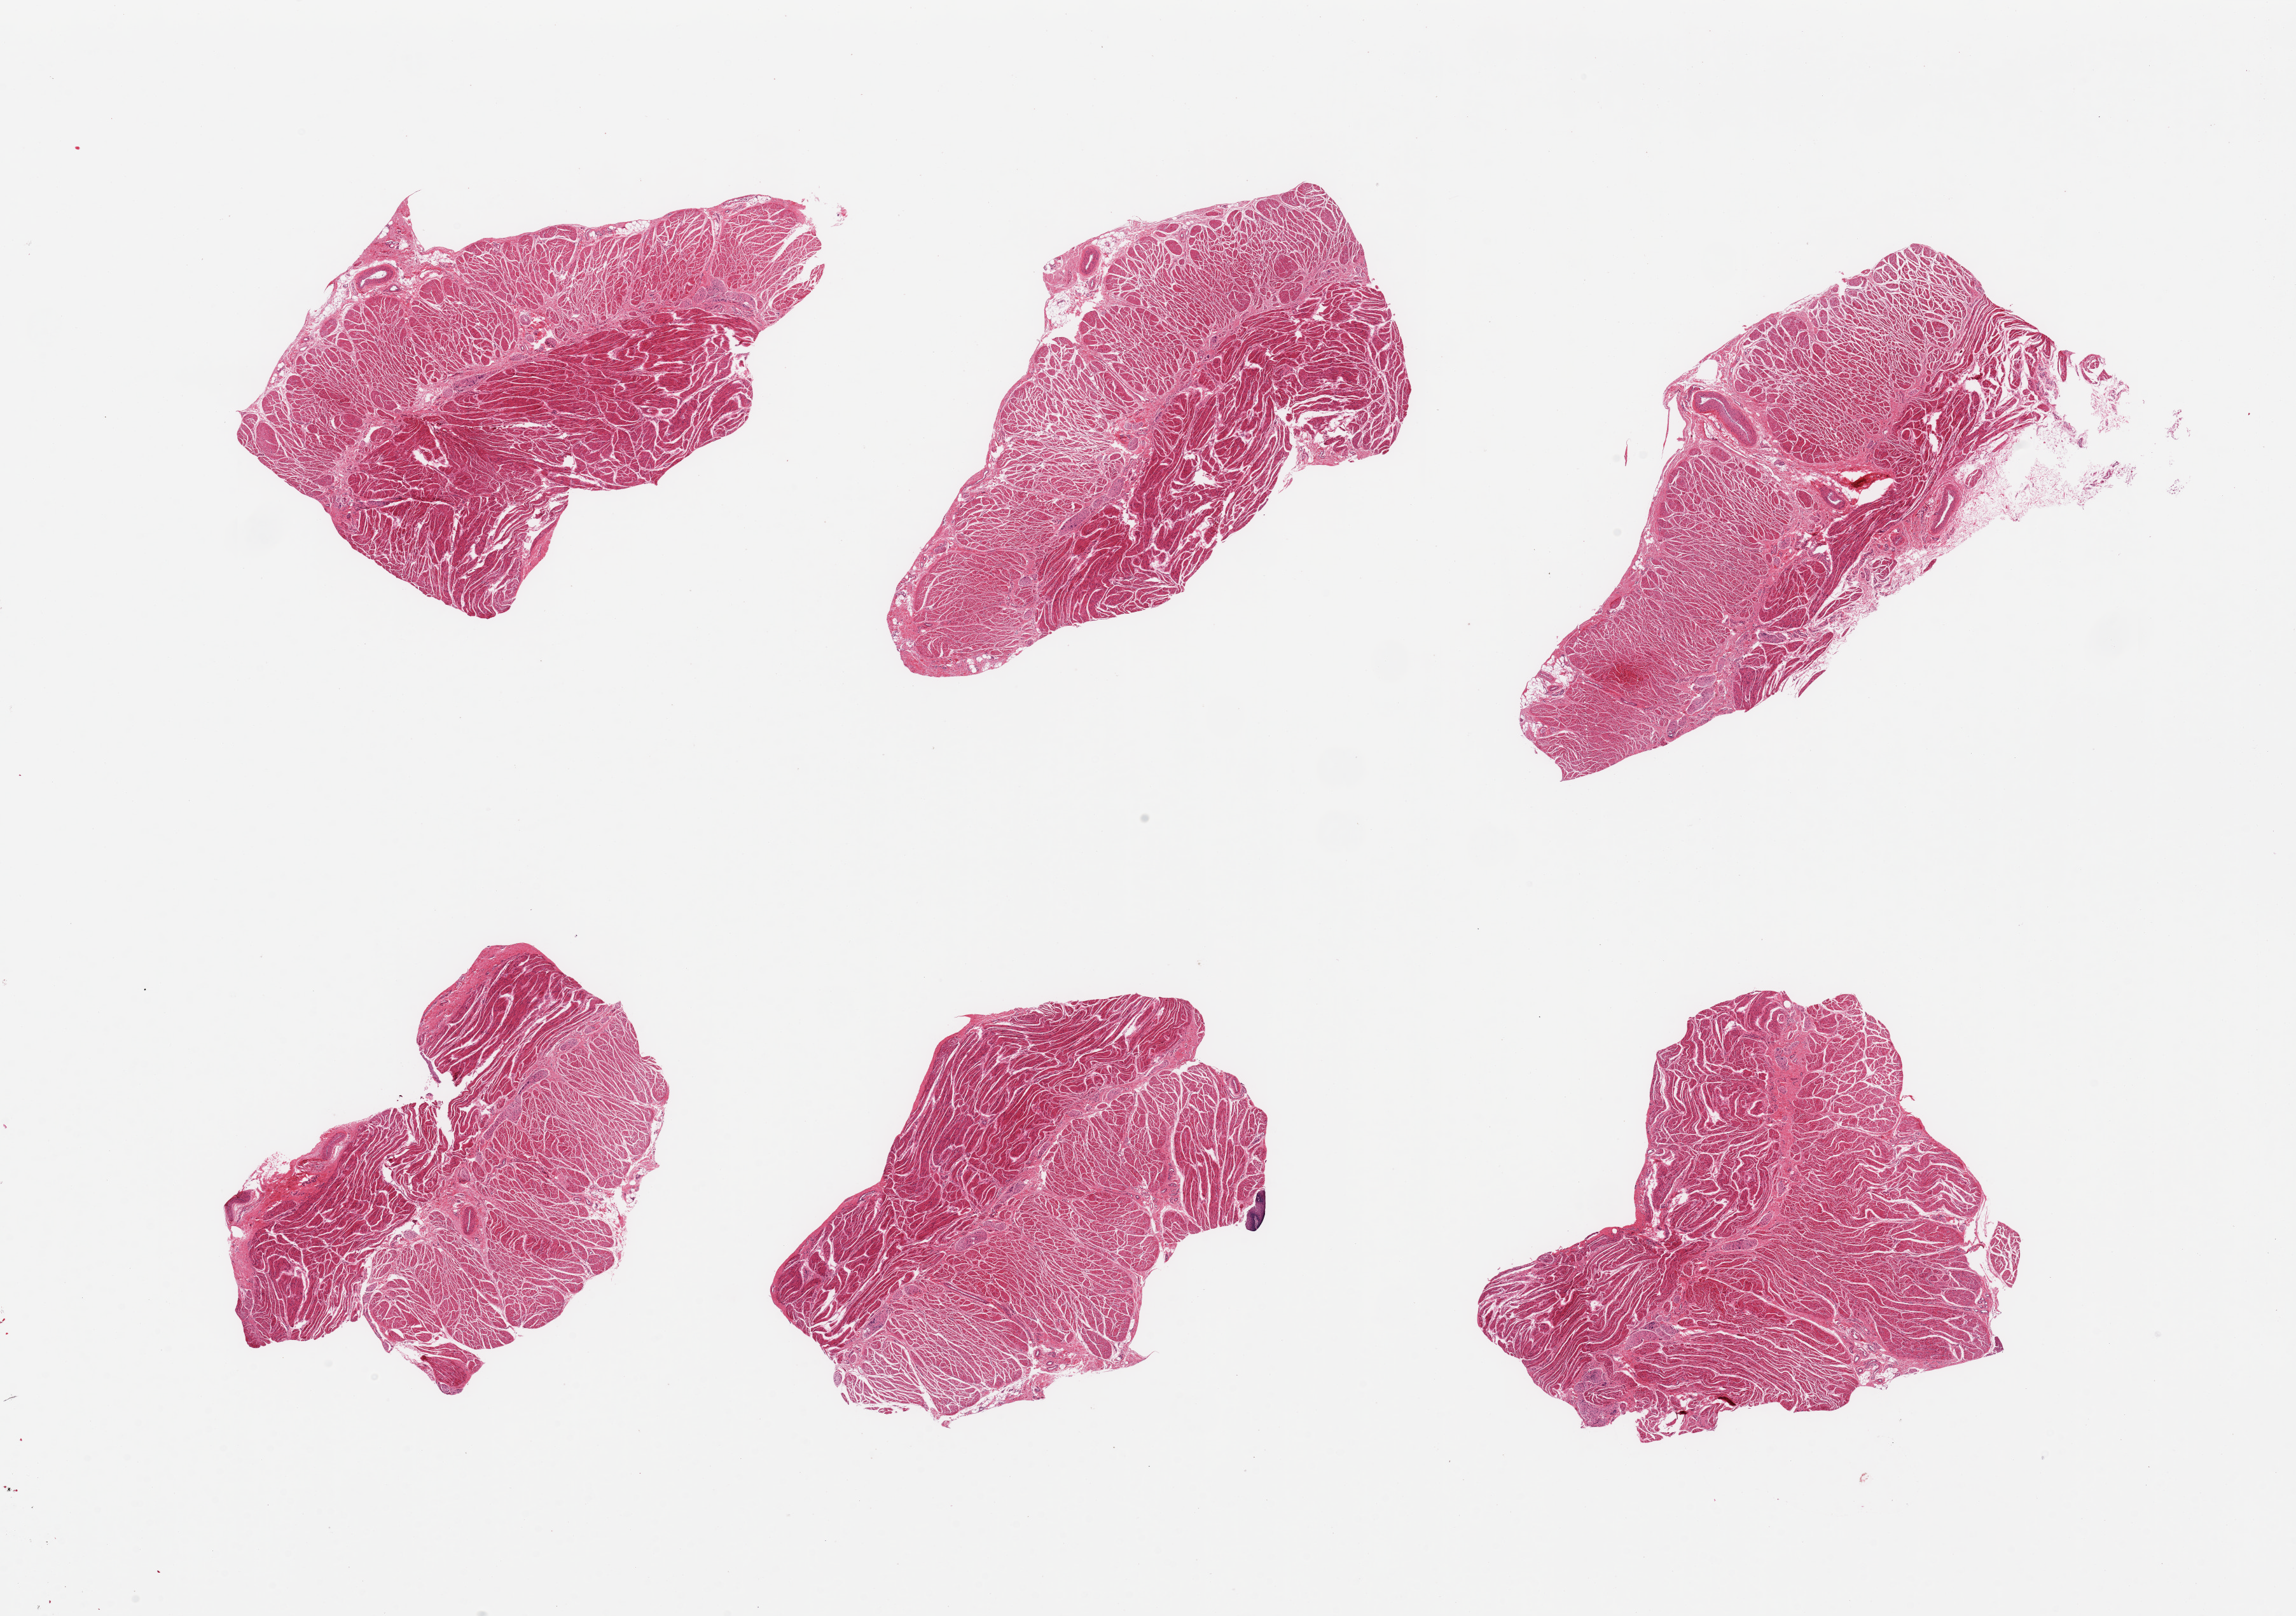
Digitized hematoxylin and eosin (H&E)-stained section, brightfield — shown as a low-resolution overview of the whole scanned area (about 28.5 x 20.1 mm, acquisition: 20x scan). PAXgene-fixed paraffin-embedded (PFPE) section. Target tissue: gastroesophageal junction. Donor tissue sample.
Review note (as recorded): 6 pieces; well dissected muscle except for a 0.5mm focus of squamous epithelium.